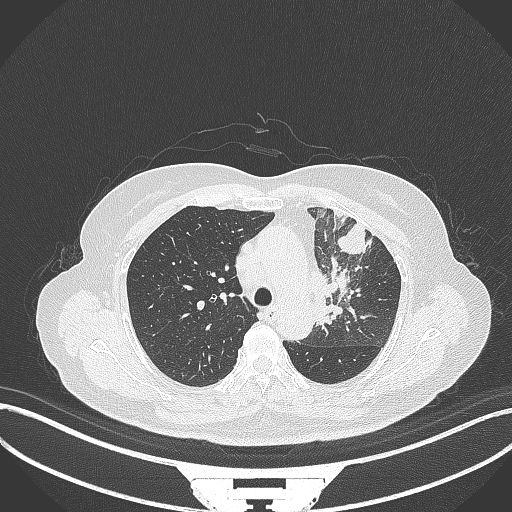
Chest CT, one axial slice; position 240 of 382 along the scan axis; reconstruction kernel B70f; 120 kVp; lung window (W 1500 / L -600 HU); 512 × 512 image matrix. Patient: female, 64 years. Case-level facts recorded for this patient, not image findings: clinical TNM (as recorded): T2a N2 M0.
Annotated regions visible in this slice (bounding box drawn by a radiologist):
- lung tumour (recorded histology: adenocarcinoma): box from (x=312, y=253) to (x=362, y=328) px
- lung tumour (recorded histology: adenocarcinoma): (x=333, y=221)–(x=370, y=253)